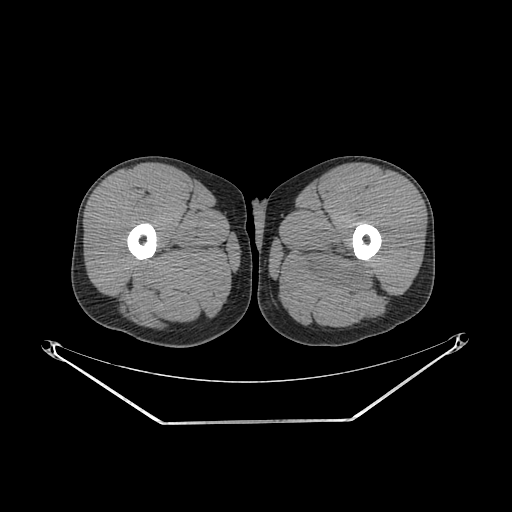
CT of an extremity soft-tissue mass (from a PET/CT study), one axial slice; position 245 of 267 along the scan axis; 140 kVp; soft-tissue window (W 400 / L 40 HU); 3.75 mm slice thickness; 512 × 512 image matrix. Male patient. From the clinical record (not read from this slice): histological type: extraskeletal osteosarcoma; grade: high; site of the primary tumour: left adductur.
Outlined on this slice (expert contour drawn on MRI and transferred to this co-registered scan by the dataset authors):
- gross tumour volume (mass): bounding box [x1, y1, x2, y2] px = [288, 238, 378, 298]